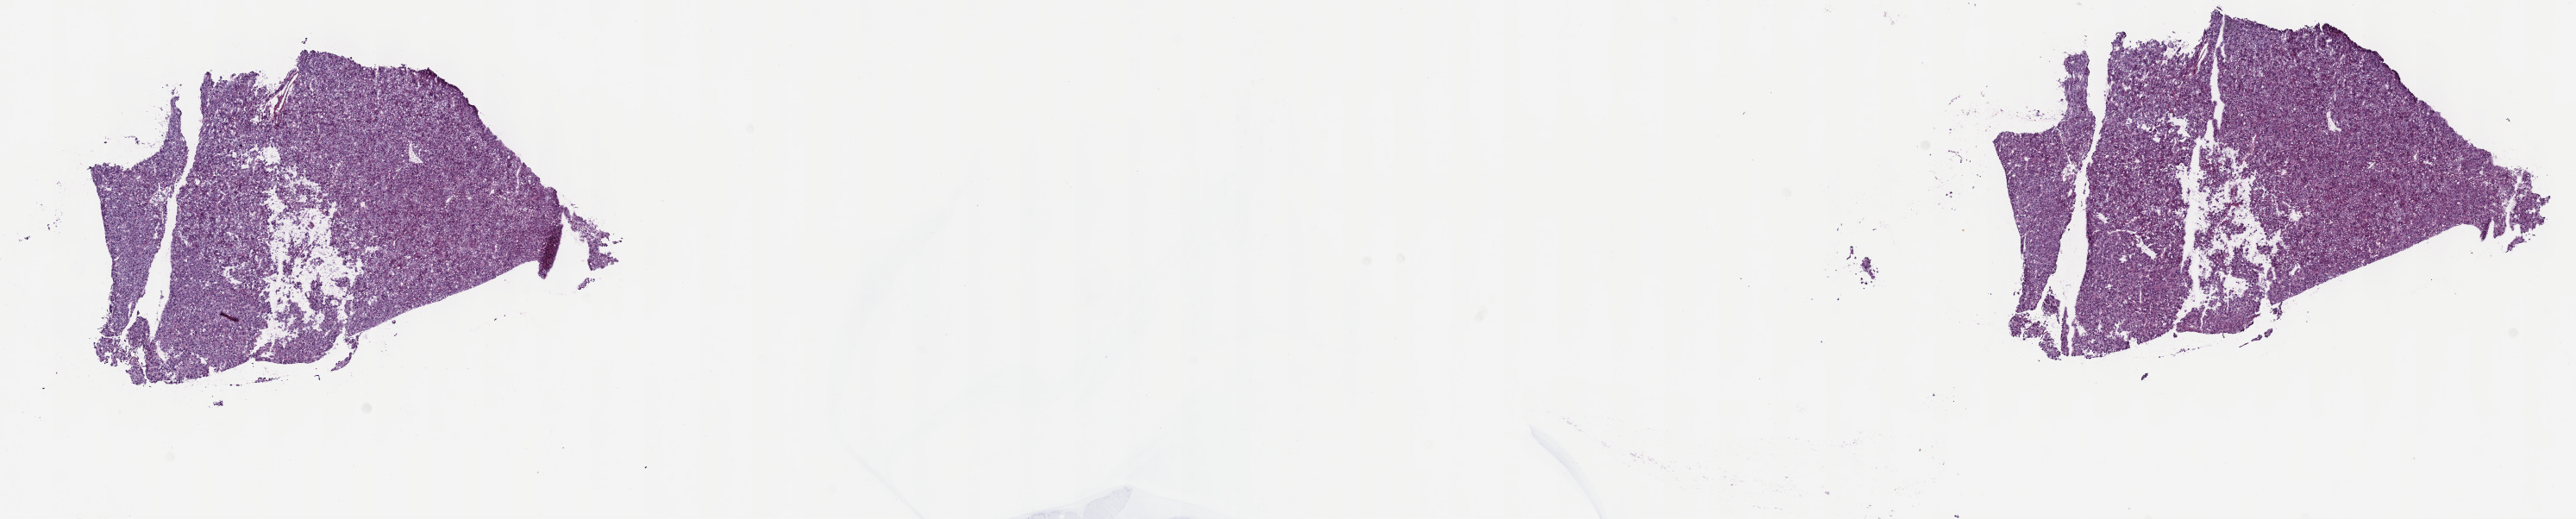
Whole-slide histology image, Hematoxylin and eosin (H&E) stained — low-resolution overview of the scanned area, about 24.2 x 4.9 mm (slide scanned at 40x), frozen section from the top of the tissue portion, liver, primary tumour sample. Female, age 55 years at initial diagnosis. Histologic grade: G2 (moderately differentiated). Composition of this section per pathologist review: tumour cells 100%, tumour nuclei 95%, normal cells 0%, stromal cells 0%, necrosis 0%. Inflammatory infiltration, as recorded: lymphocyte infiltration 0%, monocyte infiltration 0%, neutrophil infiltration 0%.
- AJCC pathologic stage: I (6th edition)
- TNM: T1 NX MX
- histologic diagnosis: Hepatocellular carcinoma, NOS